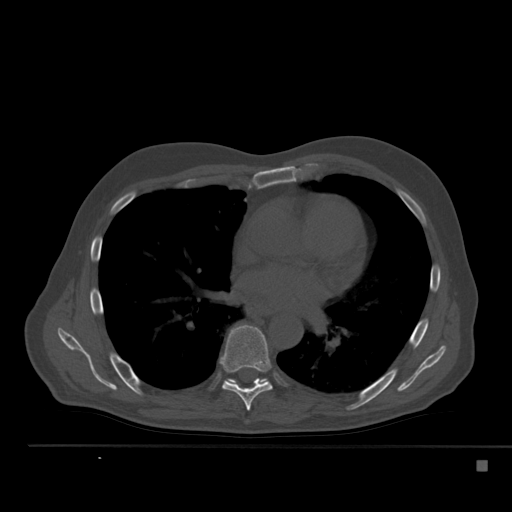
CT including the spine, one axial slice; slice 324 of 517 in the series (ordered by position); 120 kVp; bone window (W 1800 / L 400 HU); 1.5 mm slice thickness; 512 × 512 image matrix, field of view 408 × 408 mm. Patient: male, 70 years. From the clinical record (not read from this slice): primary cancer: renal.
Structures marked on this image (semi-automatic segmentation, software-assisted and operator-edited):
- T7 vertebra: bounding box [x1, y1, x2, y2] px = [220, 324, 273, 411]
- T8 vertebra: [230, 379, 262, 380]